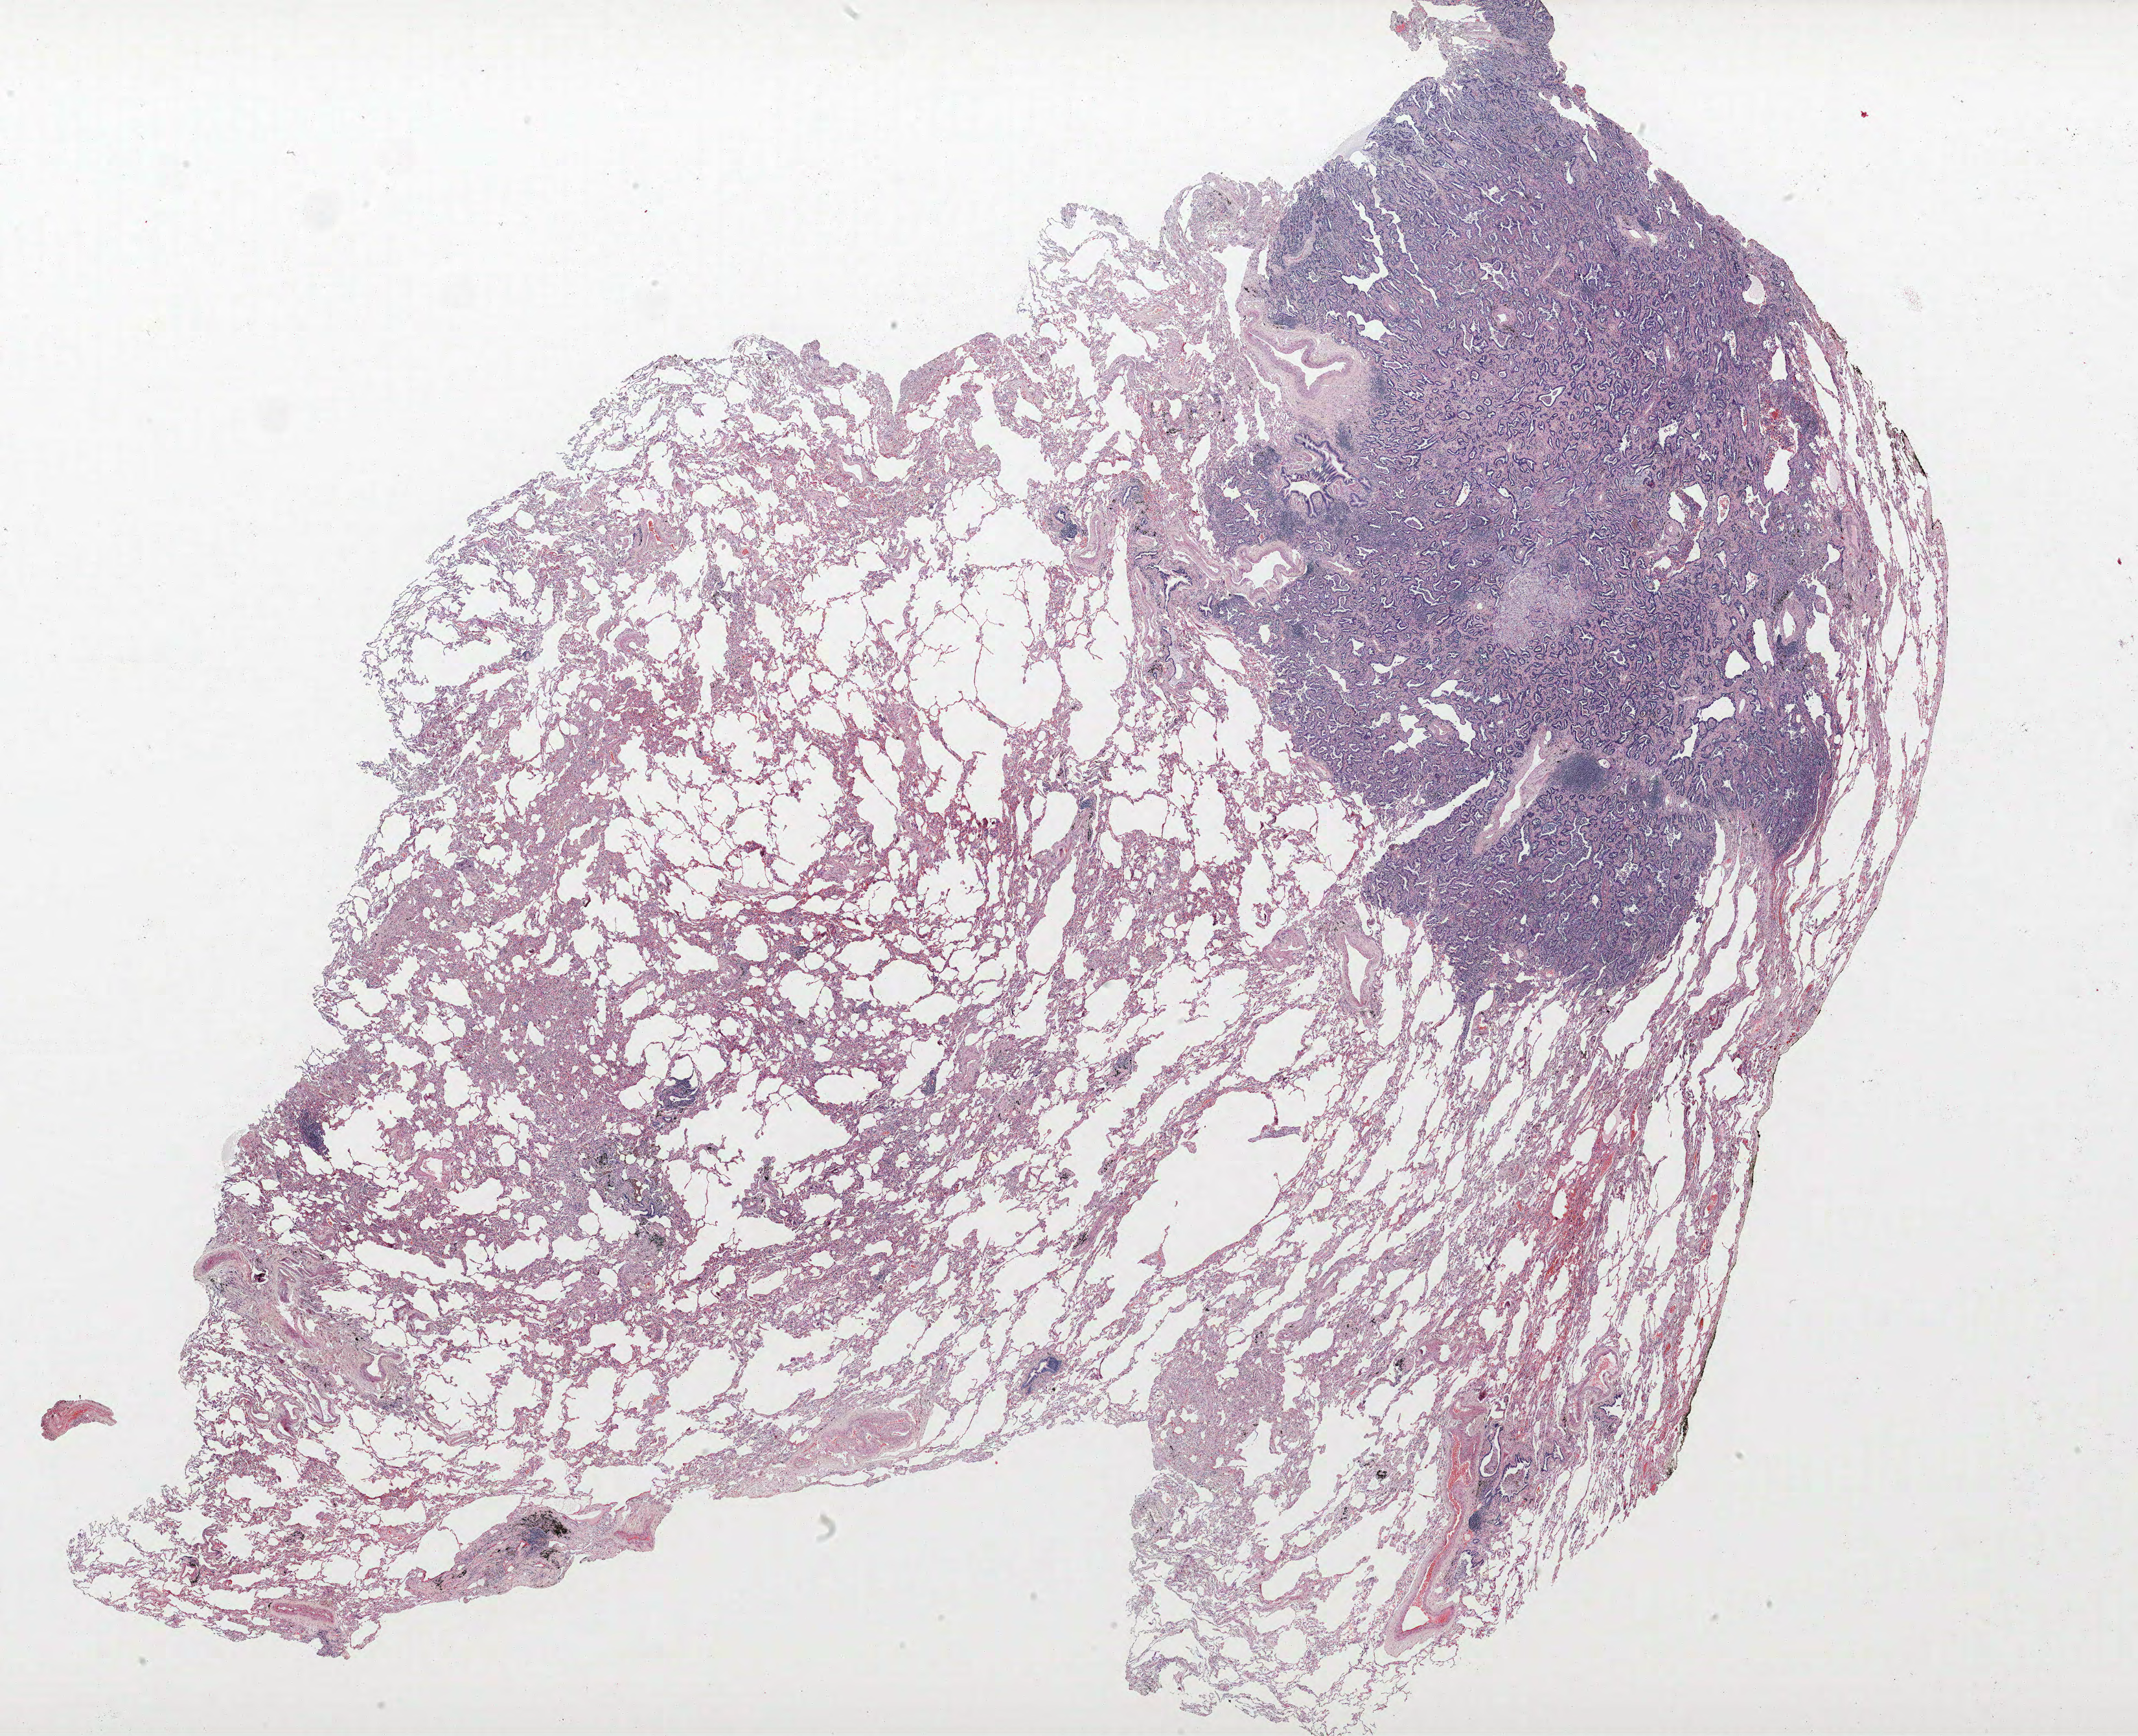
Whole-slide histology image, Hematoxylin and eosin (H&E) stained, a low-resolution overview of the entire scanned area, about 26.4 x 21.4 mm. Formalin-fixed paraffin-embedded (FFPE) section. Lung. Female patient, aged 68 at enrolment. Current smoker at enrolment.
- participant's lung-cancer diagnosis: Bronchiolo-alveolar adenocarcinoma, NOS (ICD-O-3 8250/3)
- primary tumour location (clinical record): left lower lobe
- stage (AJCC 6th edition): IIIB
- tumour size (pathology): 12 mm
- ICD-O-3 topography: lower lobe of lung (C34.3)